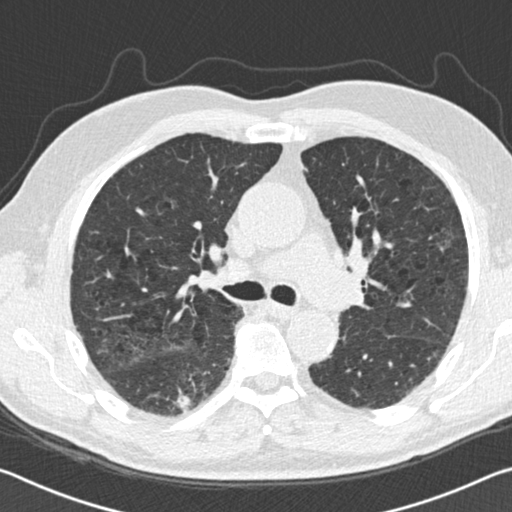
Low-dose screening chest CT, one axial slice; position 86 of 142 along the scan axis; reconstruction kernel B30f; 120 kVp; lung window (W 1500 / L -600 HU); 2 mm slice thickness; 512 × 512 image matrix.
Annotated regions visible in this slice (outlined manually by an expert reader):
- lesion 1 (tumor, lower lobe of right lung): box from (x=173, y=388) to (x=192, y=414) px